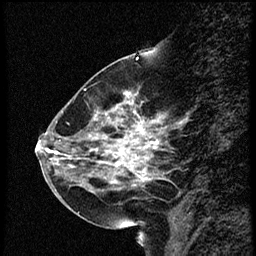
Breast MRI (dynamic contrast-enhanced), one sagittal slice. Slice 19 of 56 in the series (ordered by position). Dynamic contrast-enhanced study with each time point stored as its own series, time point 2 of 4 at this slice position (early post-contrast, ordered by acquisition time). 1.5 T. TE 4.2 ms, TR 18.9 ms. 2 mm slice thickness. 256 × 256 image matrix, field of view 200 × 200 mm. Female patient. Case-level facts recorded for this patient, not image findings: setting: breast cancer imaged before/during neoadjuvant chemotherapy; receptor status: HER2-positive.
Annotated regions visible in this slice (semi-automatic segmentation, software-assisted and operator-edited):
- analysis volume of interest (the breast-tissue region the enhancement analysis was run in; not a lesion): bounding box [x1, y1, x2, y2] px = [63, 80, 169, 215]
- tumour enhancement mask (voxels above the 100 % enhancement threshold inside the analysis volume of interest): [95, 94, 159, 183]